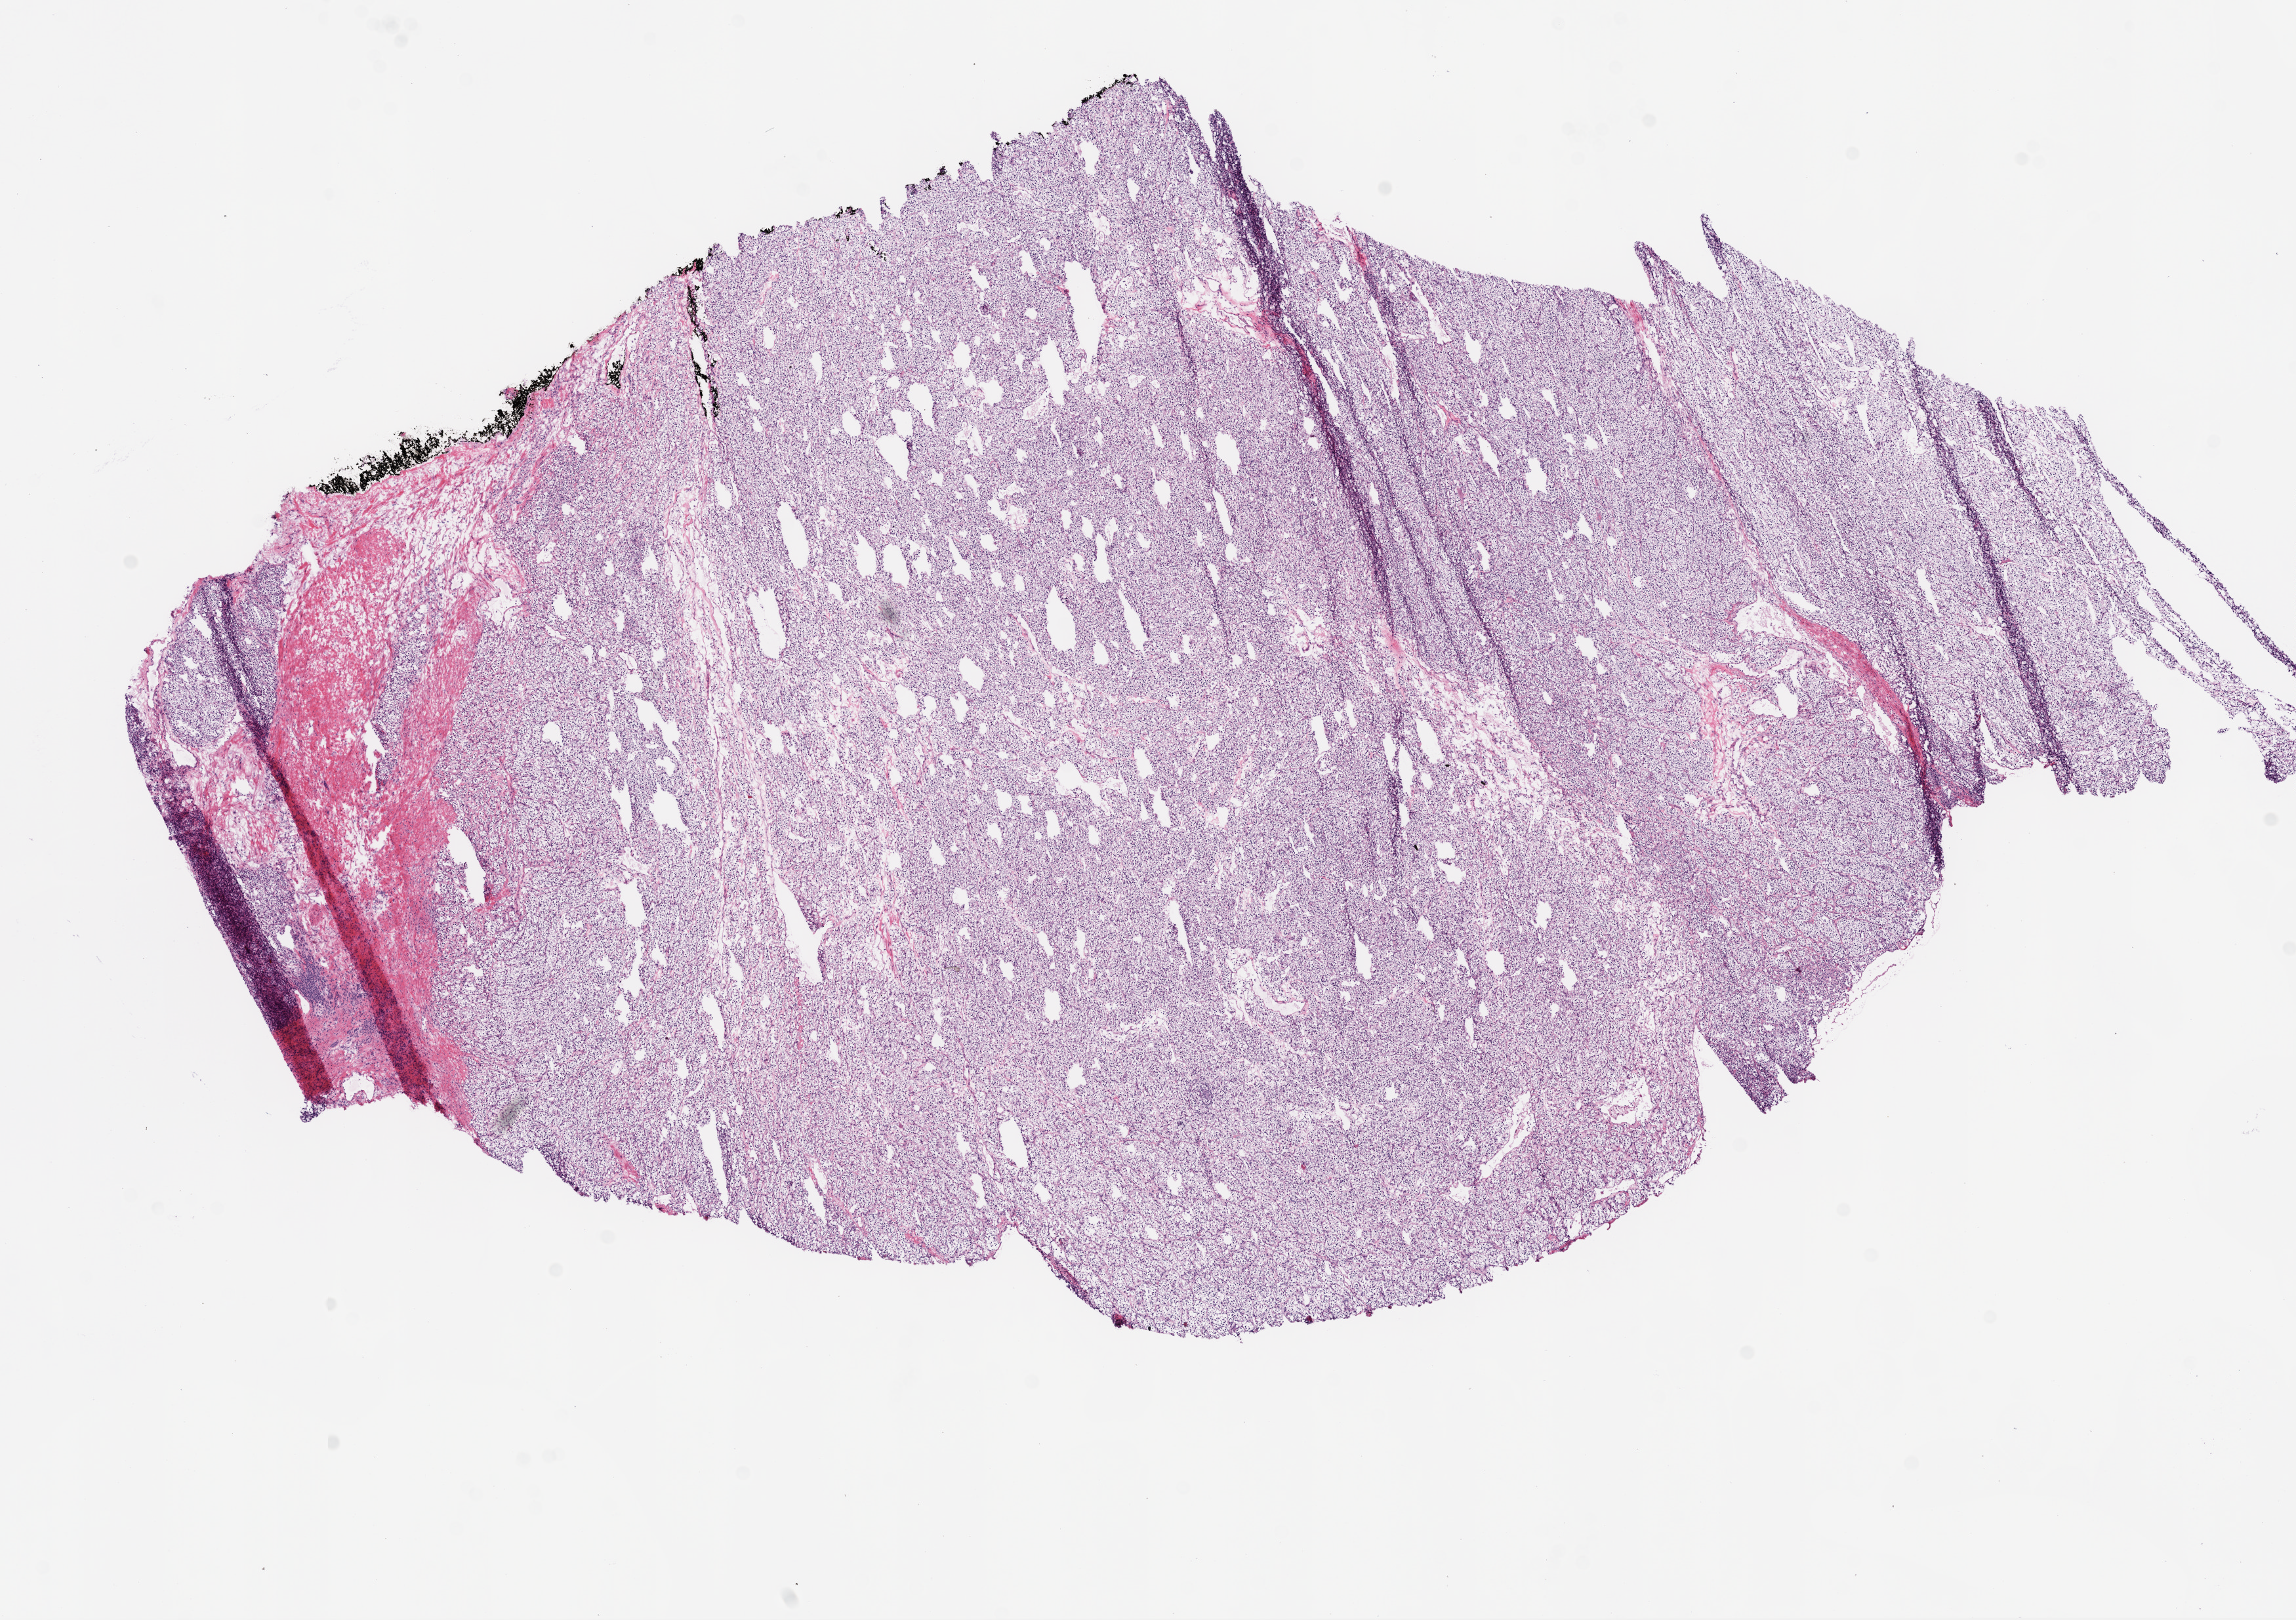
Digitized H&E tissue section (whole slide), low-resolution overview of the scanned area, about 14.0 x 9.9 mm (slide scanned at 20x). Frozen section. Primary tumour sample from the kidney. Female patient; age at initial diagnosis 52 years. Histologic grade: G1 (well differentiated). Slide review estimates, as recorded: tumour cells 90%, tumour nuclei 90%, normal cells 0%, stromal cells 10%, necrosis 0%.
* TNM: T1b NX M0
* AJCC pathologic stage: I
* pathologic diagnosis: Clear cell adenocarcinoma, NOS